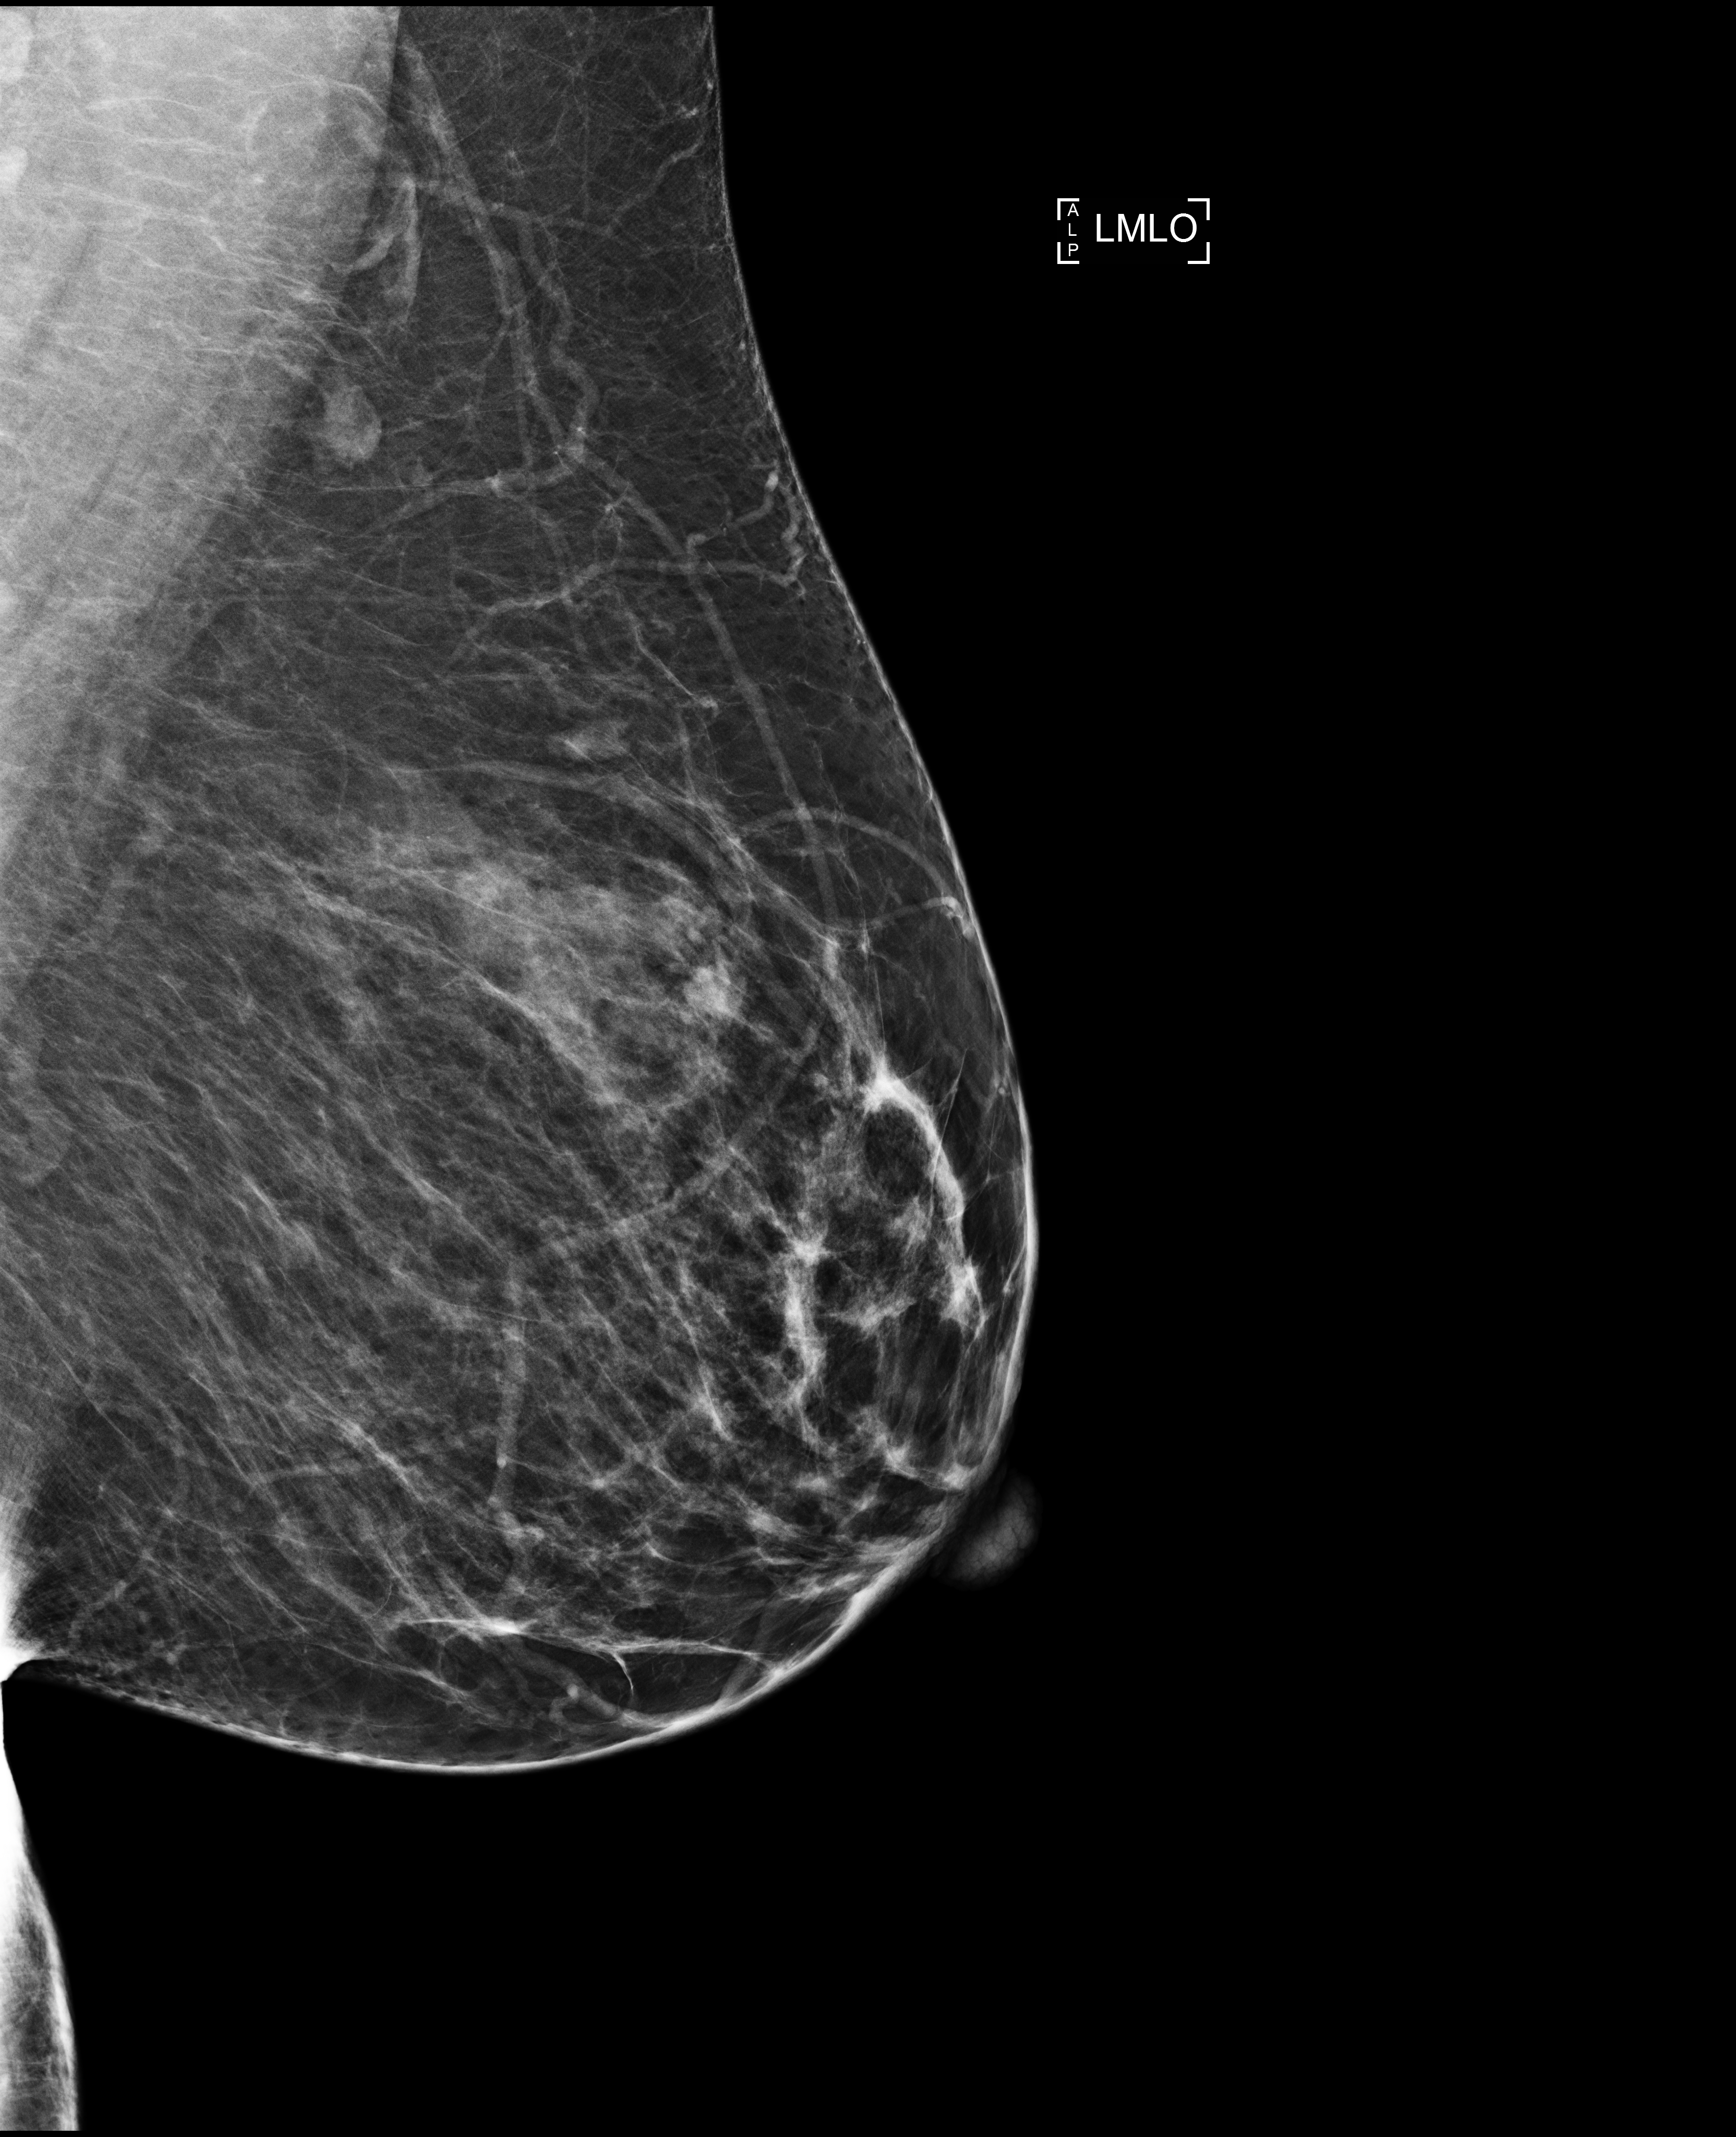
Full-field digital mammogram (FFDM); left breast; MLO view; screening examination. Patient aged 52 years (female).
- breast density at the screening exam (both breasts): heterogeneously dense (BI-RADS density category c)
- final BI-RADS category for the screening round (tomosynthesis exam, both breasts): category 1
- recall: no recall after this screen